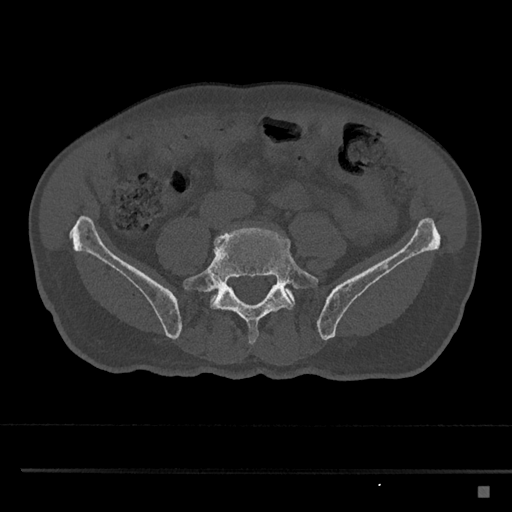
CT including the spine, one axial slice. Position 581 of 797 along the scan axis. Reconstruction kernel Br40s/3. 120 kVp. Bone window (W 1800 / L 400 HU). 0.5 mm slice thickness. 512 × 512 image matrix, field of view 391 × 391 mm. Male patient, age 59 years. Case-level facts recorded for this patient, not image findings: primary cancer: prostate.
Annotated regions visible in this slice (semi-automatically segmented with operator editing):
- L5 vertebra: bounding box (x1, y1, x2, y2) in pixels: (183, 227, 318, 345)